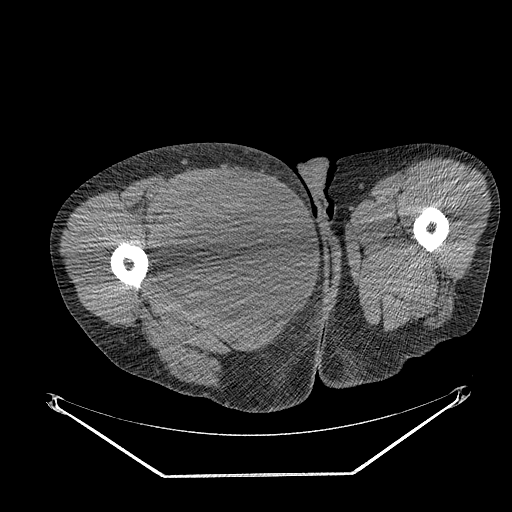
CT of an extremity soft-tissue mass (from a PET/CT study), one axial slice; position 270 of 311 along the scan axis; 140 kVp; soft-tissue window (W 400 / L 40 HU); 3.75 mm slice thickness; 512 × 512 image matrix, field of view 500 × 500 mm. Male patient. From the clinical record (not read from this slice): histological type: undifferentiated - pleiomorphic; grade: high; site of the primary tumour: right thigh.
Outlined on this slice (expert contour drawn on MRI and transferred to this co-registered scan by the dataset authors):
- gross tumour volume including surrounding oedema: bounding box [x1, y1, x2, y2] px = [158, 171, 268, 279]
- gross tumour volume (mass): [158, 171, 268, 279]